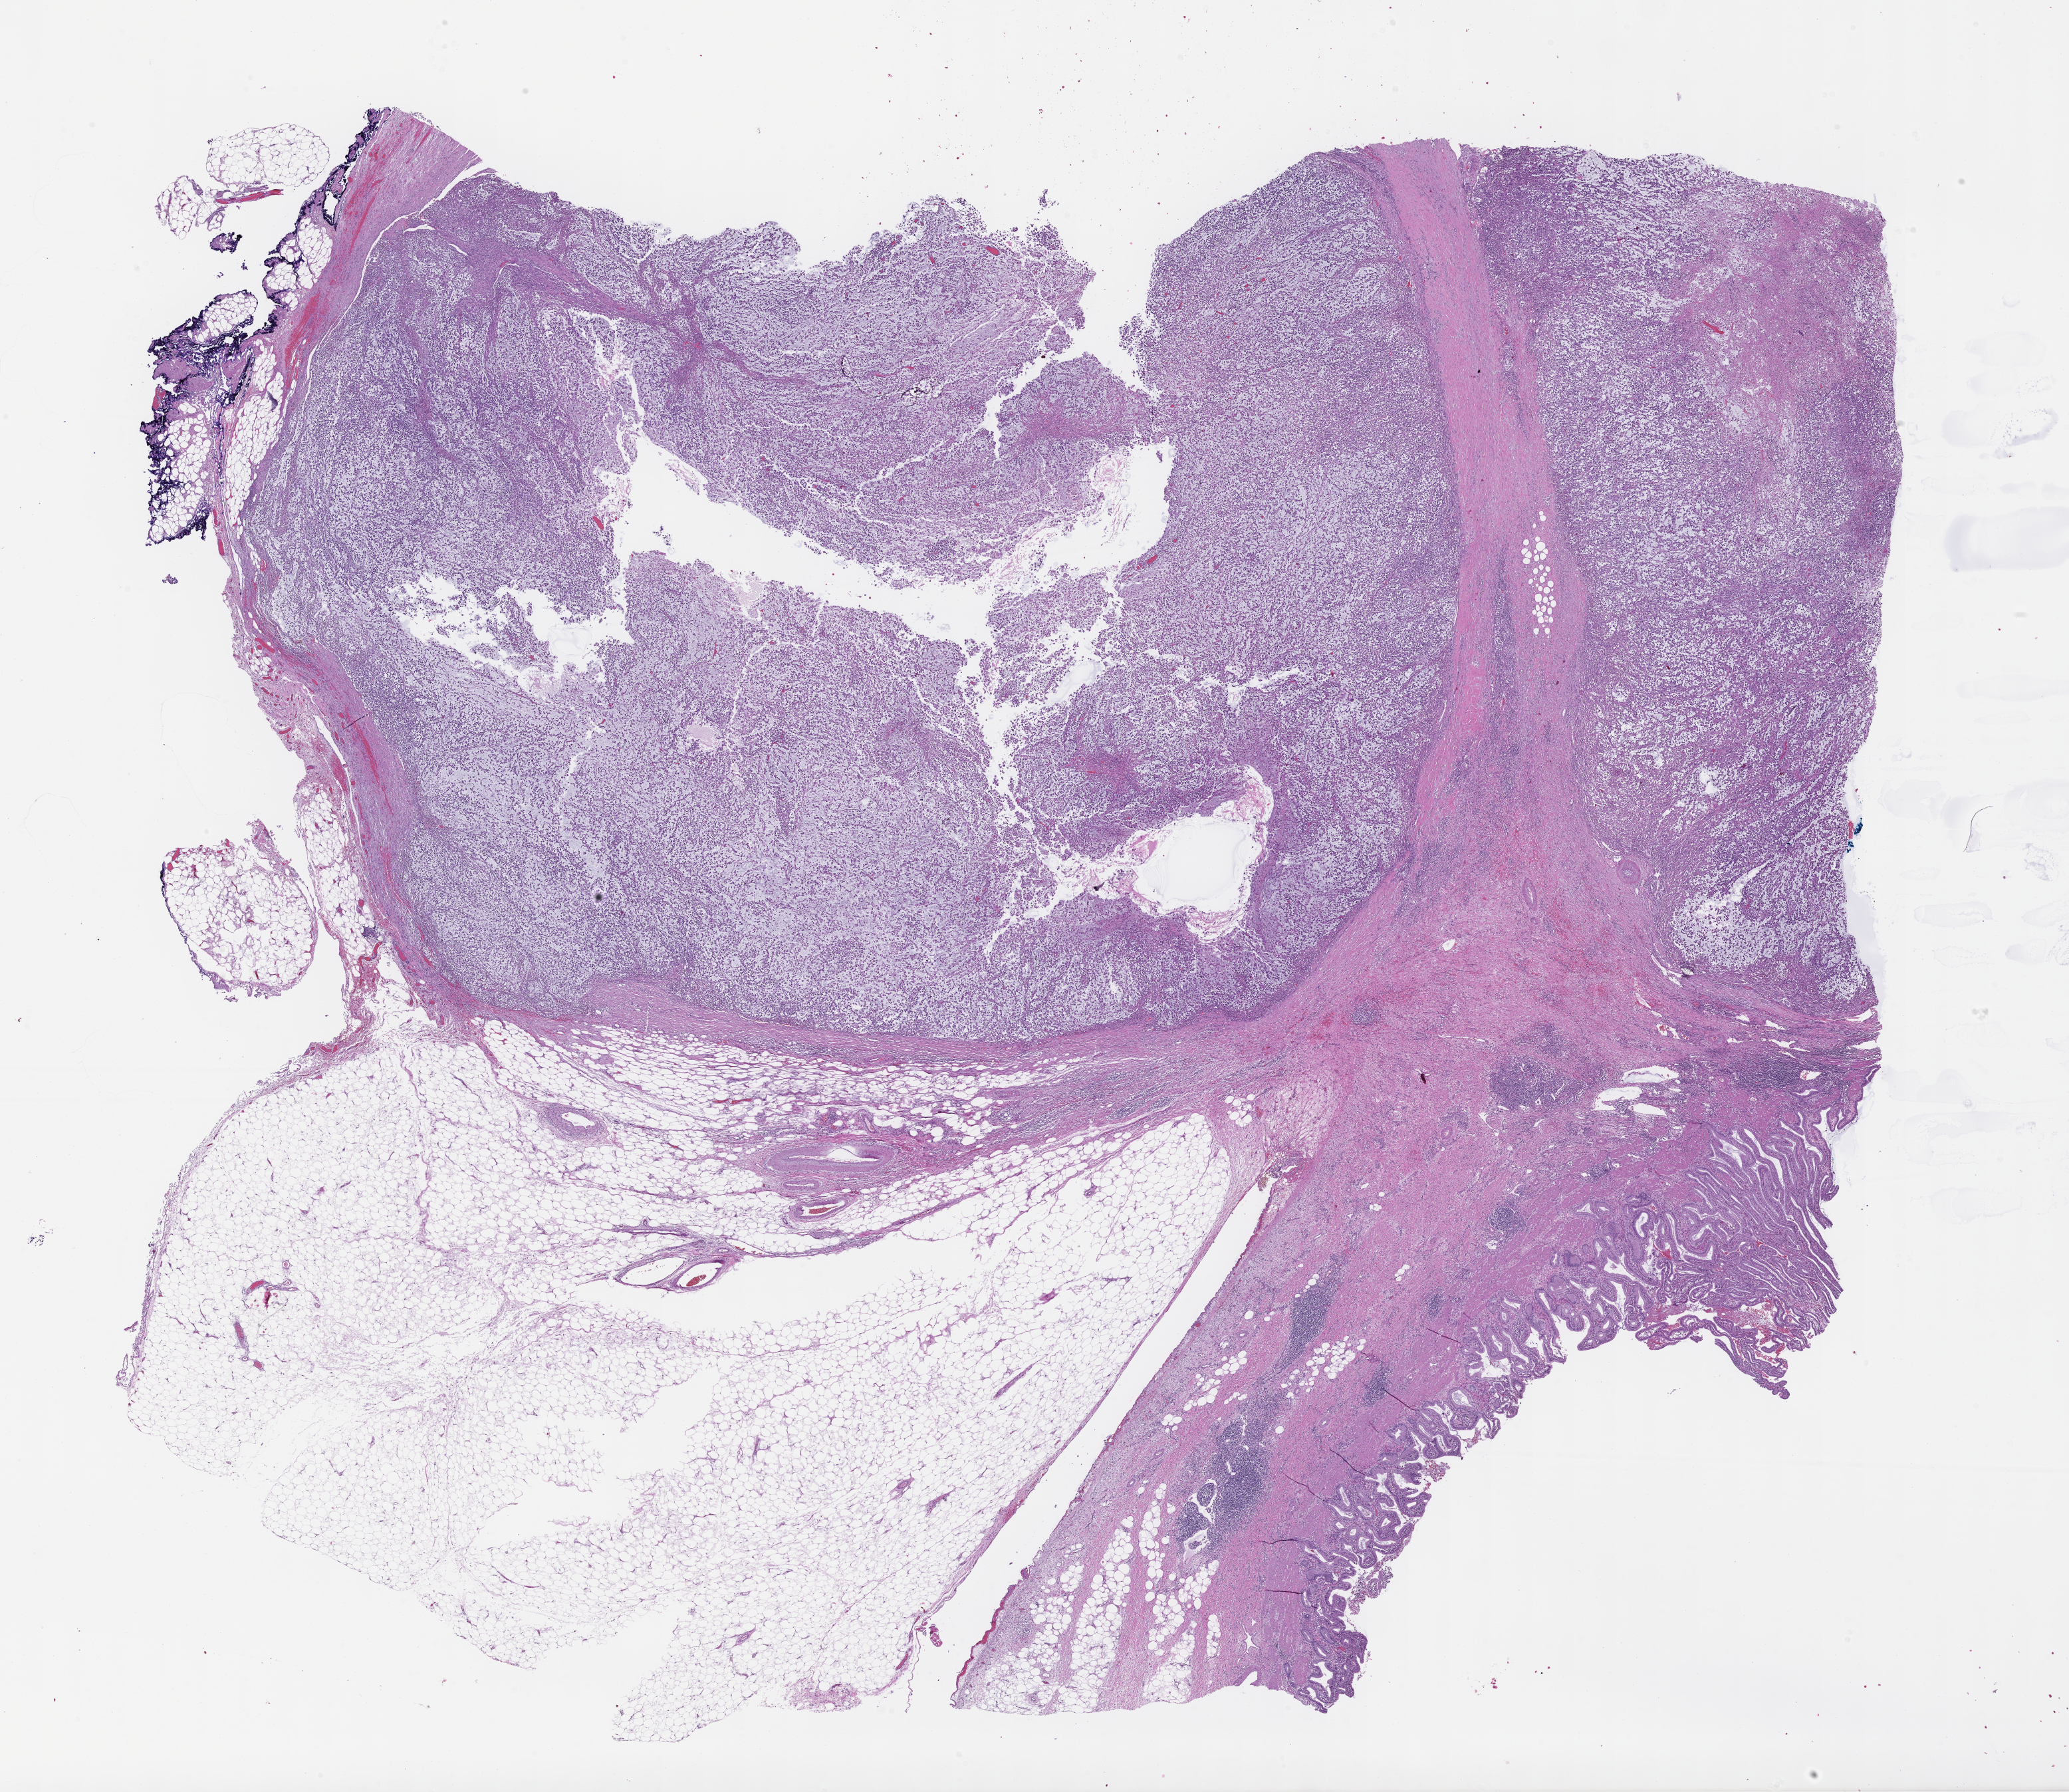
Whole-slide image, haematoxylin and eosin stain, shown as a low-resolution overview of the whole scanned area (about 25.1 x 21.8 mm), FFPE section. Patient sex: male.
This section: metastasis (sampled organ not recorded). Primary diagnosis of the patient: Melanoma.